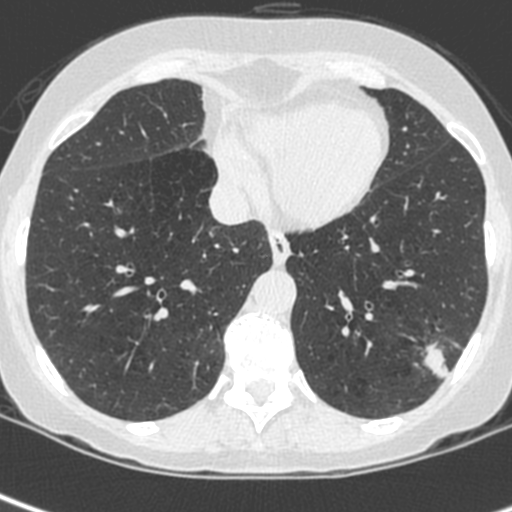
Axial slice from a low-dose chest CT screening exam; baseline screening round; lung window (W 1500 / L -600 HU); 1.3 mm slice thickness; standard (soft-tissue) reconstruction kernel (C); slice 161 of 252 in the series; 512 × 512 image matrix, field of view 271 × 271 mm. Female, age 56 years at enrolment. Current smoker at enrolment.
Expert-annotated lung lesion, bounding box [x1, y1, x2, y2] px = [411, 331, 471, 390]. Reader record for this screening exam (exam-level; its link to the box is not recorded): non-calcified nodule or mass ≥4 mm, left lower lobe, 37 × 29 mm, spiculated (stellate) margins, ground glass attenuation. Lung cancer was diagnosed 91 days after this screen: squamous cell carcinoma, NOS, left lower lobe, poorly differentiated (G3), stage IIIA (AJCC 6th edition), 35 mm at pathology.